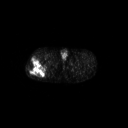
FDG PET of an extremity soft-tissue mass (from a PET/CT study), one axial slice. Slice 259 of 267 in the series (ordered by position). 128 × 128 image matrix, field of view 700 × 700 mm. Patient: male, 43 years. From the clinical record (not read from this slice): histological type: poorly differentiated synovial sarcoma; grade: high; site of the primary tumour: right buttock.
Outlined on this slice (expert contour drawn on MRI and transferred to this co-registered scan by the dataset authors):
- gross tumour volume including surrounding oedema: box from (x=27, y=57) to (x=48, y=78) px
- gross tumour volume (mass): (x=27, y=57)–(x=47, y=78)